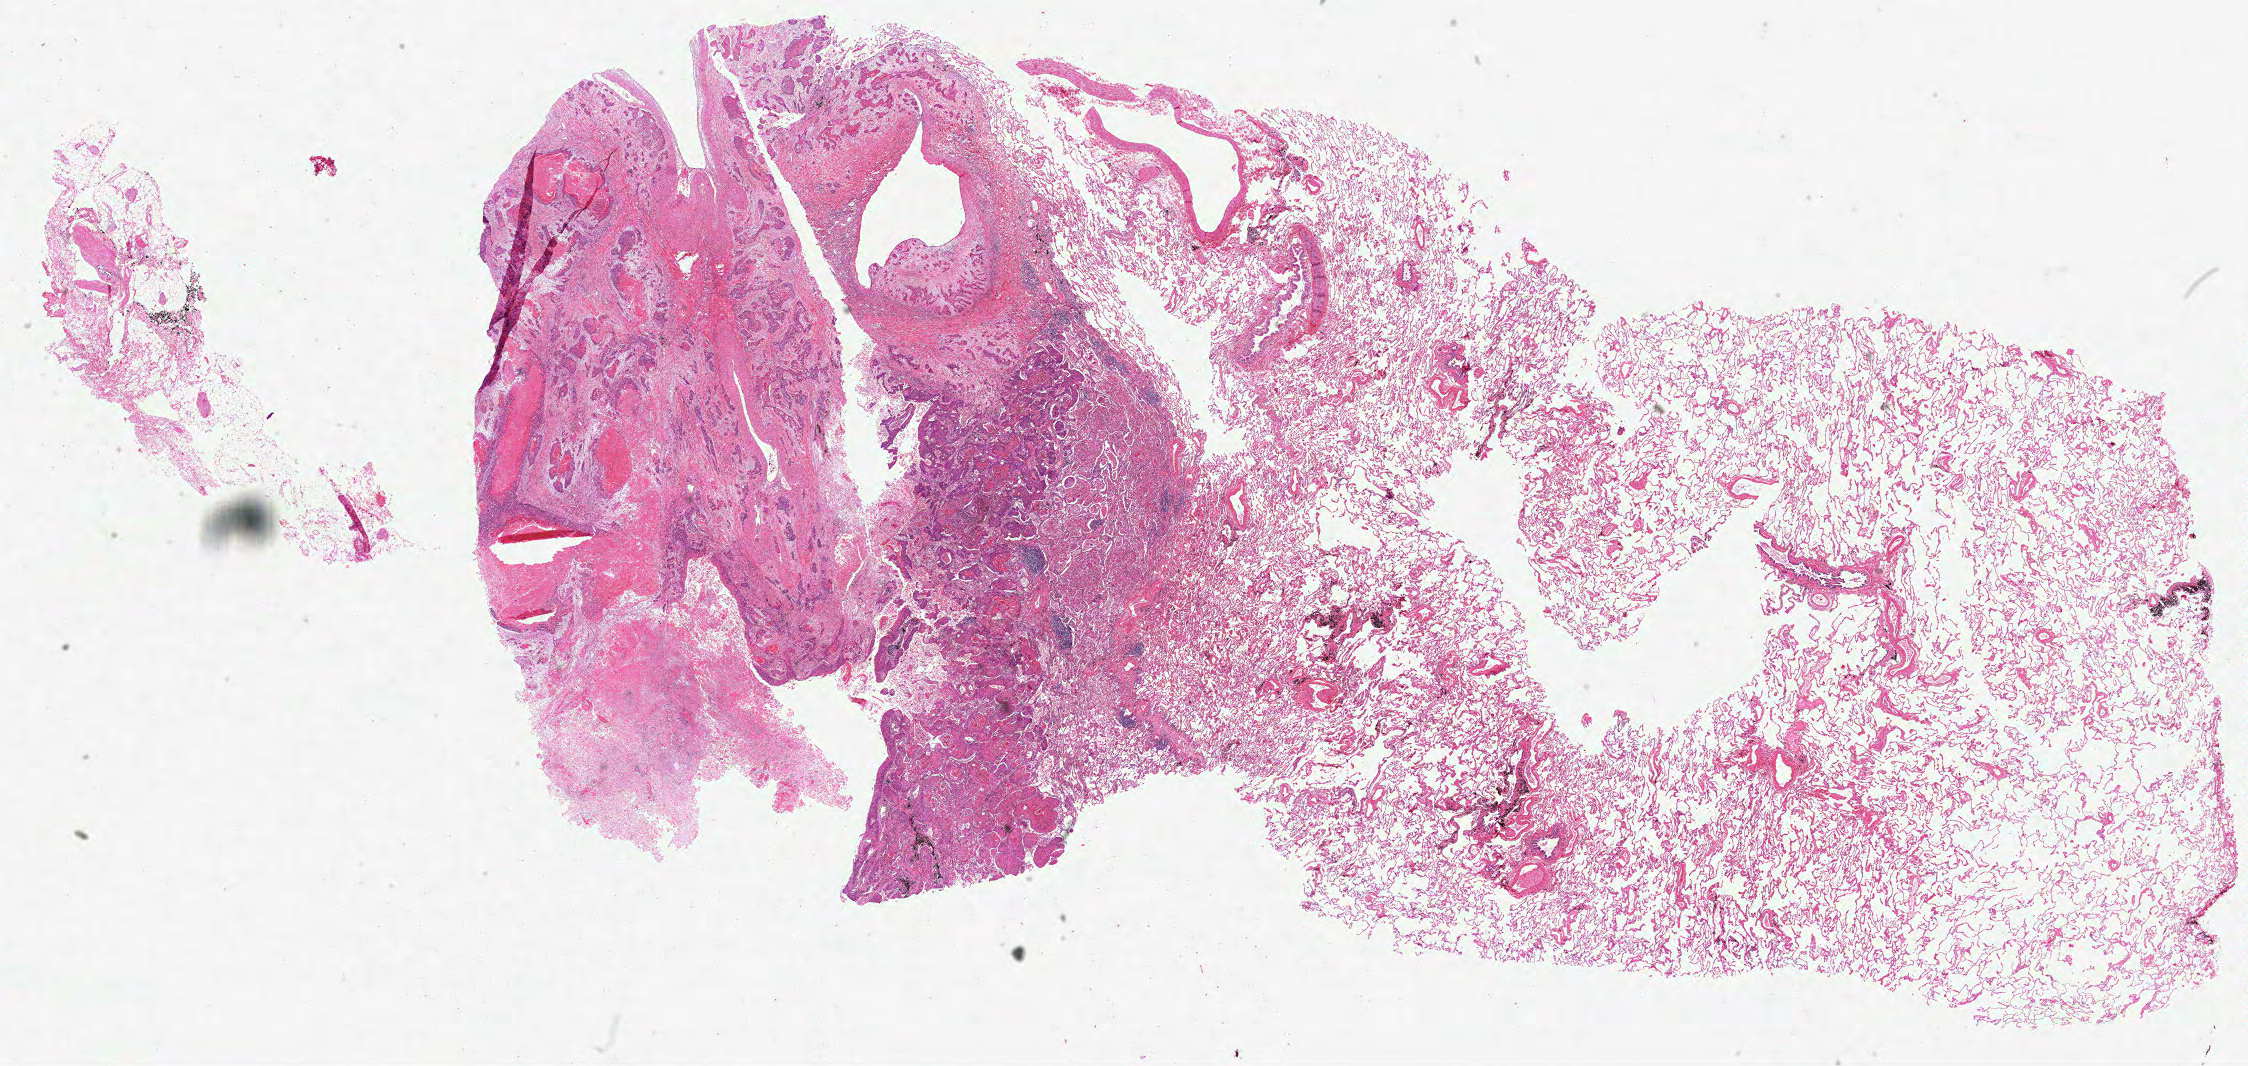
Whole-slide histology image, H&E-stained, a low-resolution overview of the entire scanned area, about 36.3 x 17.2 mm (acquisition: 40x scan), formalin-fixed paraffin-embedded (FFPE) diagnostic section, lung, primary tumour sample. Male, age 64 years at initial diagnosis.
Diagnosis: Squamous cell carcinoma, NOS (upper lobe, lung). TNM: T2 N0 M0. Laterality: right. AJCC pathologic stage: IB.